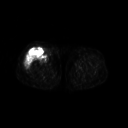
FDG PET of an extremity soft-tissue mass (from a PET/CT study), one axial slice. Slice 234 of 311 in the series (ordered by position). 3.27 mm slice thickness. 128 × 128 image matrix, field of view 500 × 500 mm. Patient: female, 57 years. From the clinical record (not read from this slice): histological type: pleiomorphic undifferentiated sarcoma; grade: high; site of the primary tumour: right quadricep.
Structures marked on this image (expert contour drawn on MRI and transferred to this co-registered scan by the dataset authors):
- tumour plus oedema (research contour): bounding box <25,49,46,71> (left, top, right, bottom; pixels)
- tumour (research contour): <25,49,46,71>